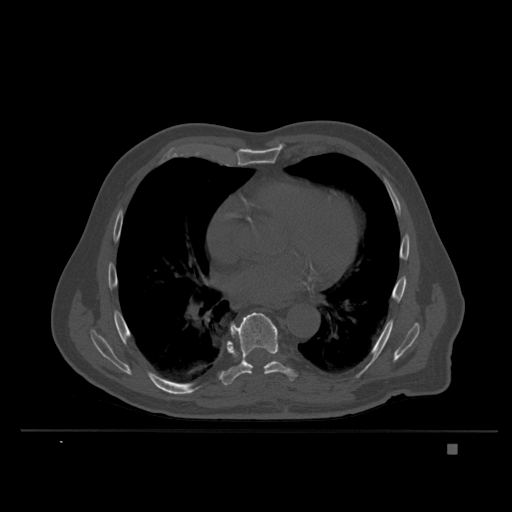
CT including the spine, one axial slice. Position 230 of 435 along the scan axis. Bone window (W 1800 / L 400 HU). 1.5 mm slice thickness. 512 × 512 image matrix. Patient: male, 73 years. Case-level facts recorded for this patient, not image findings: primary cancer: skin.
Structures marked on this image (semi-automatically segmented with operator editing):
- T7 vertebra: box from (x=230, y=325) to (x=236, y=335) px
- T8 vertebra: (x=220, y=312)–(x=297, y=386)